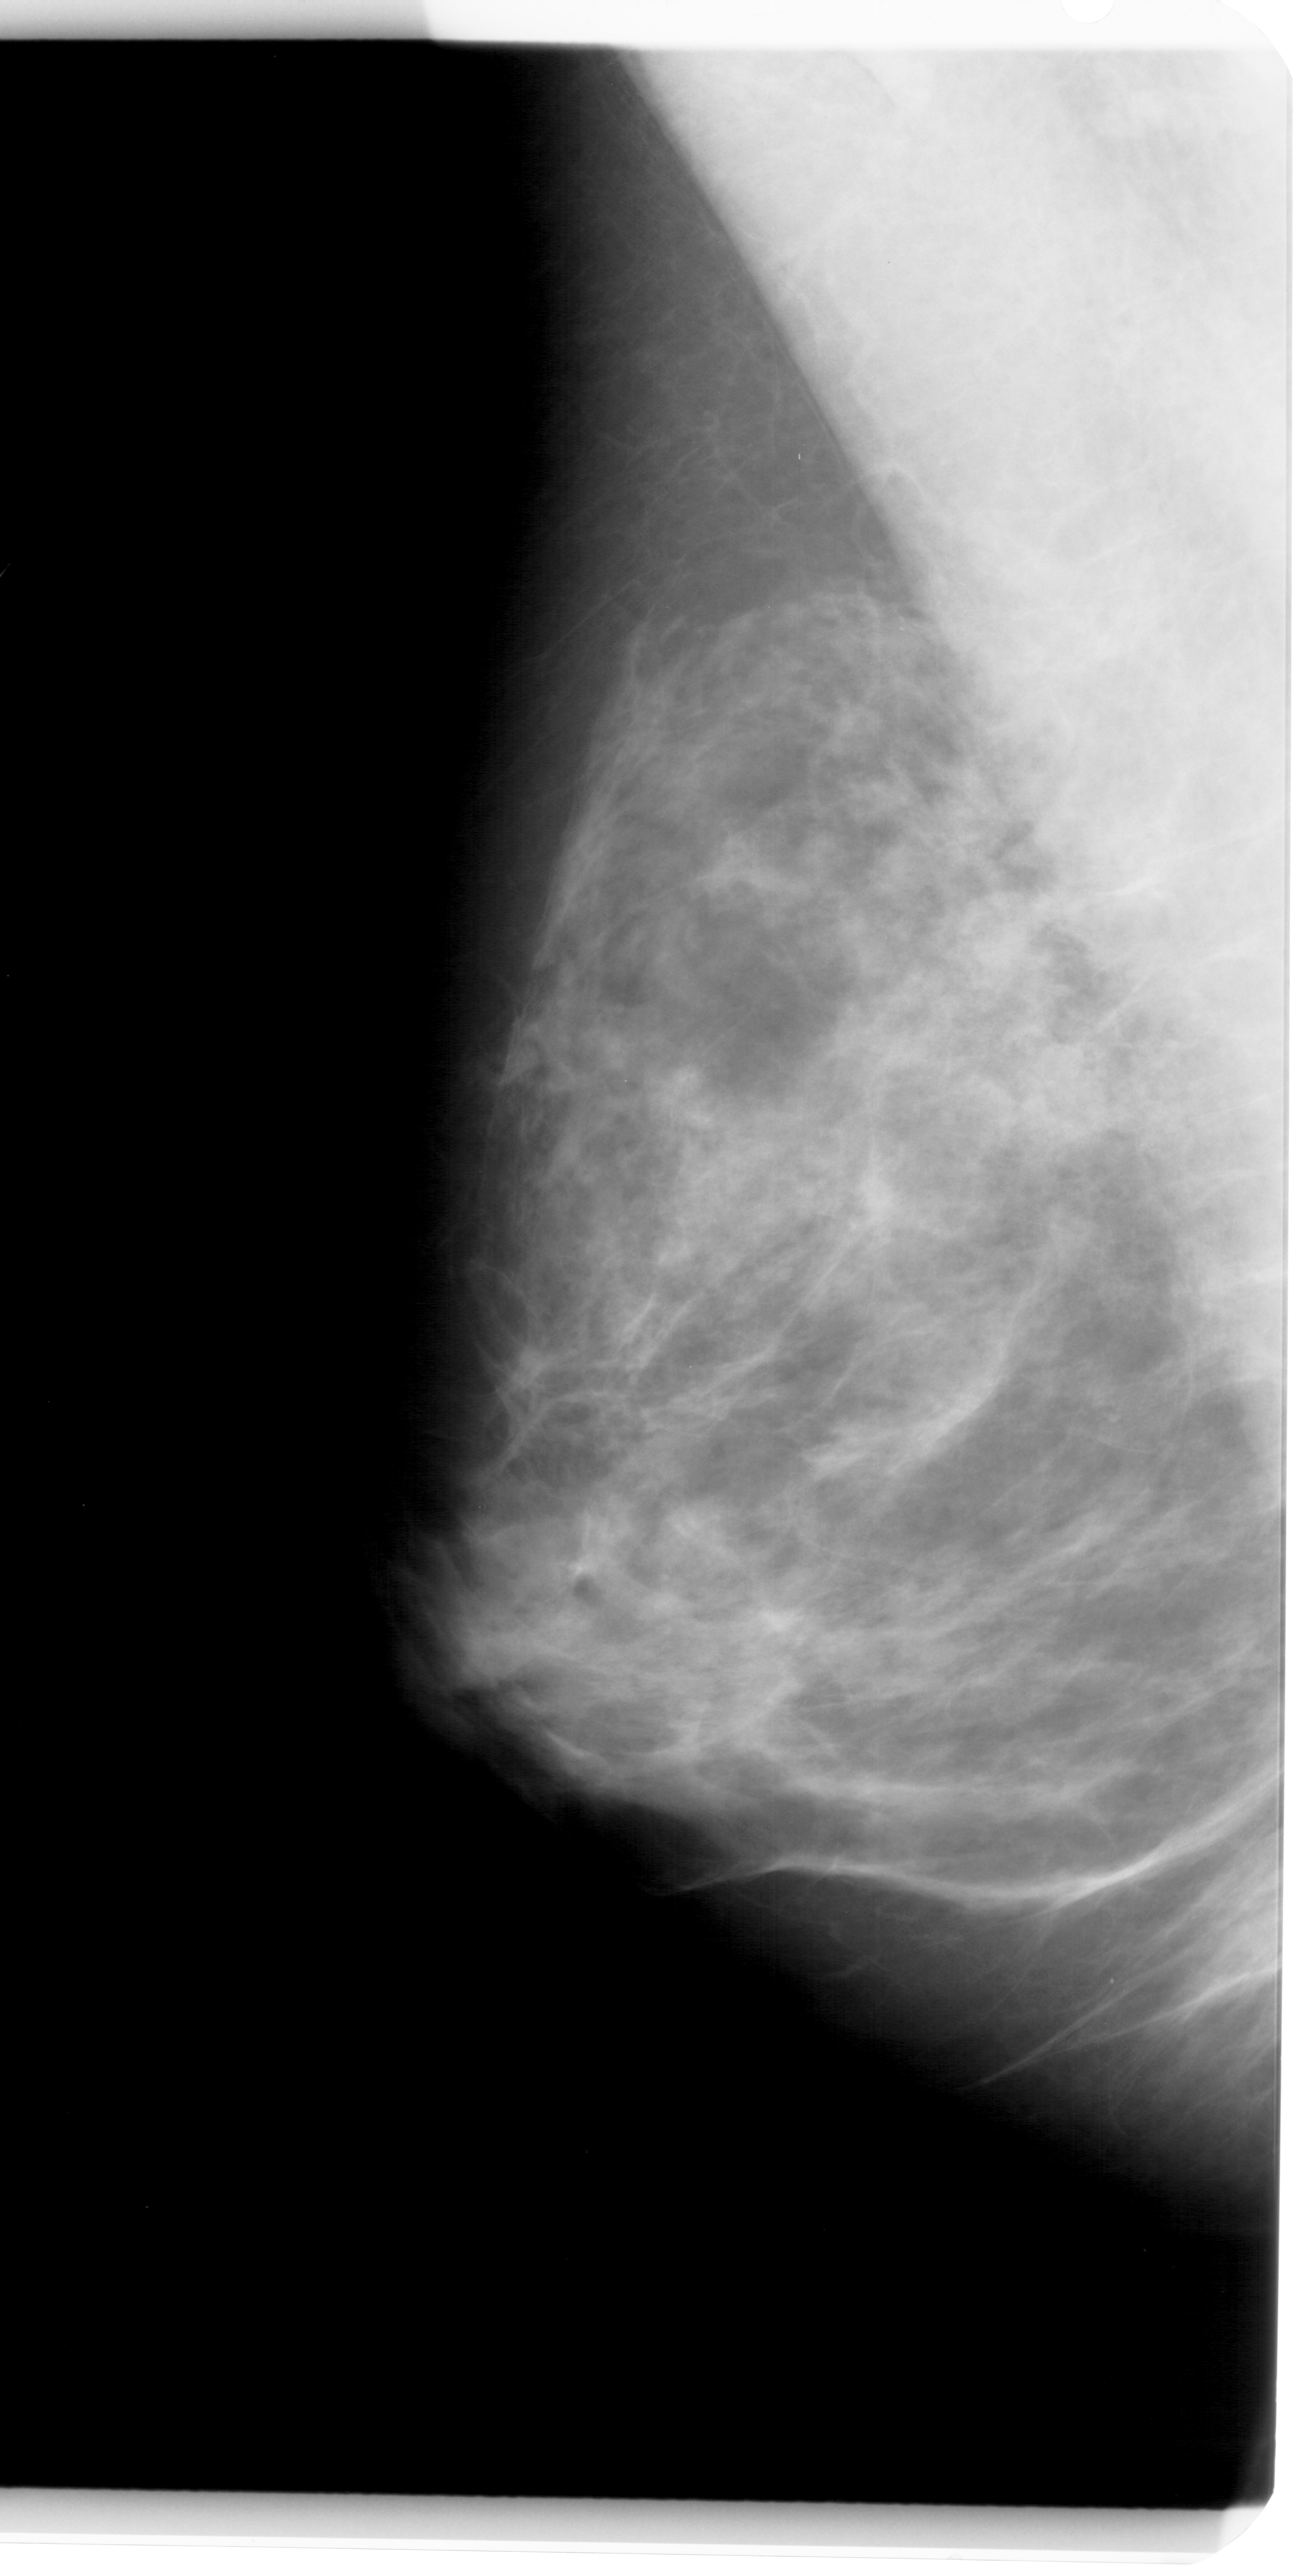
Scanned film-screen mammogram, left breast, mediolateral oblique (MLO) view.
- Finding: calcifications, morphology pleomorphic, distribution clustered; BI-RADS assessment category 3; pathology result (as recorded, not read from the image): benign.